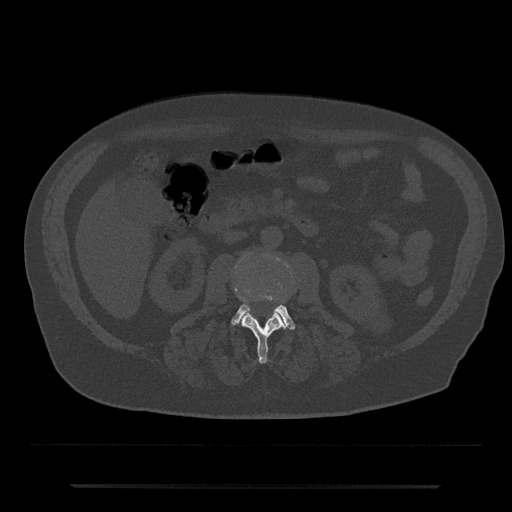
CT including the spine, one axial slice. Slice 444 of 797 in the series (ordered by position). Reconstruction kernel Br40s/3. 120 kVp. Bone window (W 1800 / L 400 HU). 0.5 mm slice thickness. 512 × 512 image matrix, field of view 434 × 434 mm. Patient: male, 80 years. From the clinical record (not read from this slice): primary cancer: prostate; vertebrae with lytic lesions (as recorded): L1, T11.
Outlined on this slice (semi-automatic segmentation, software-assisted and operator-edited):
- L2 vertebra: box from (x=241, y=294) to (x=288, y=364) px
- L3 vertebra: (x=231, y=293)–(x=295, y=330)